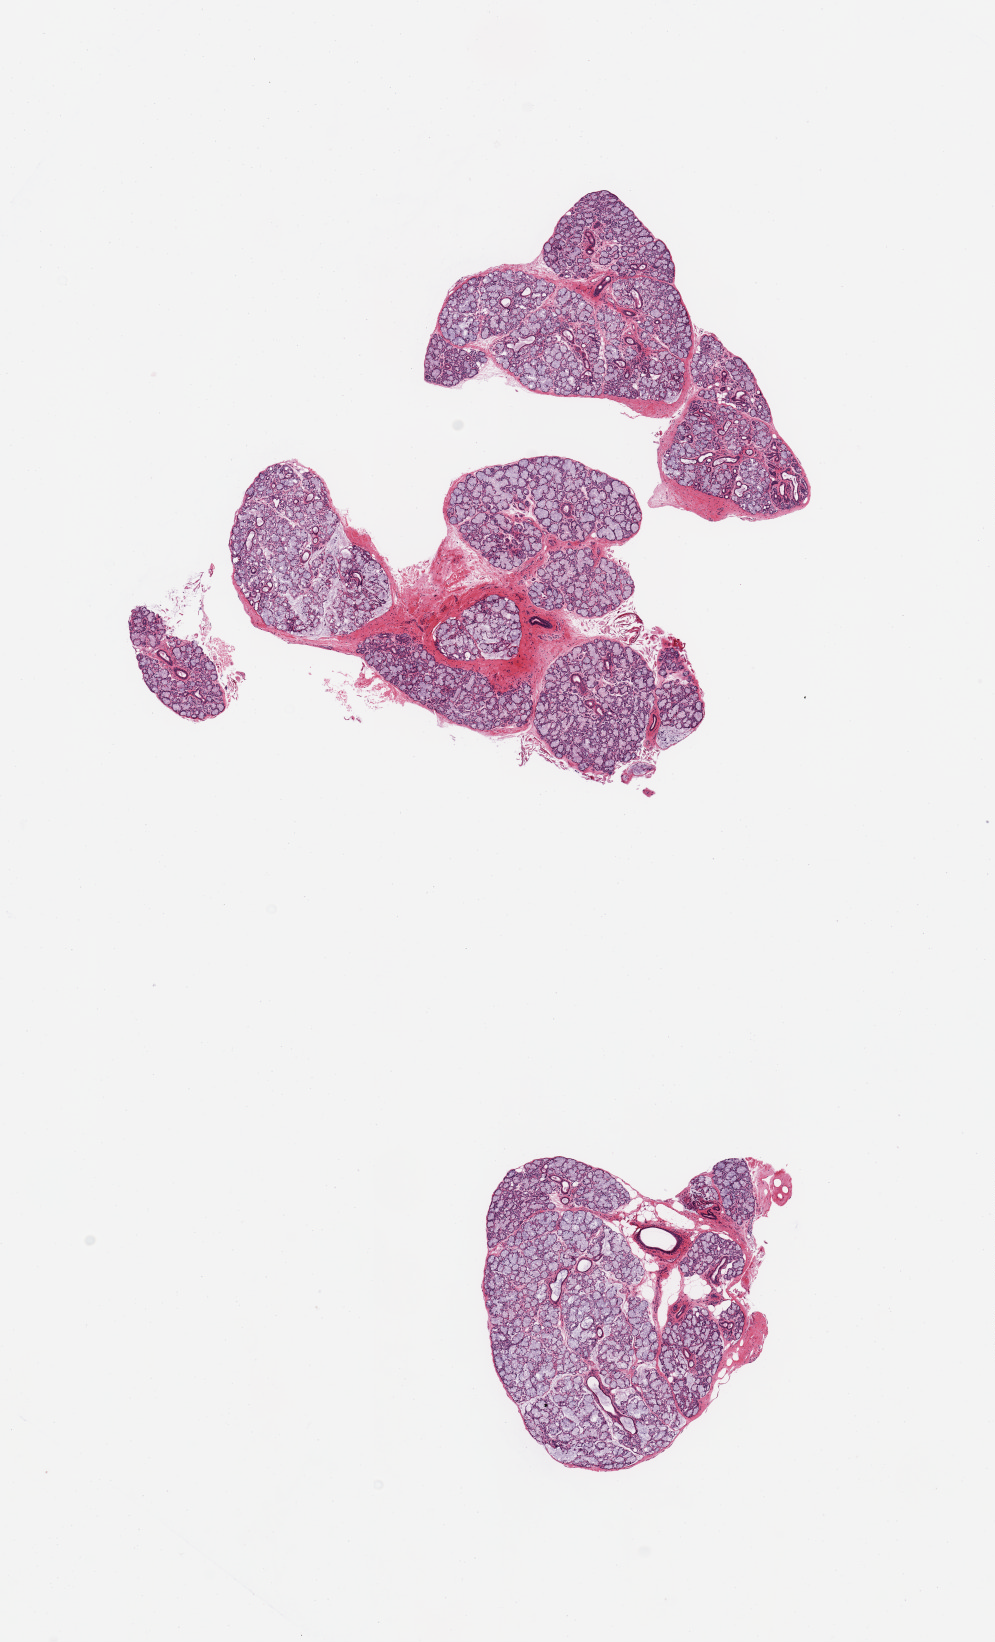
Hematoxylin and eosin (H&E) whole-slide image, a low-resolution overview of the entire scanned area, about 7.9 x 13.0 mm; PAXgene-fixed paraffin-embedded (PFPE) section; sampled site (target tissue): minor salivary gland; tissue donor sample. Male donor.
Pathologist's review note for this sample: 2 pieces; well trimmed salivary gland.